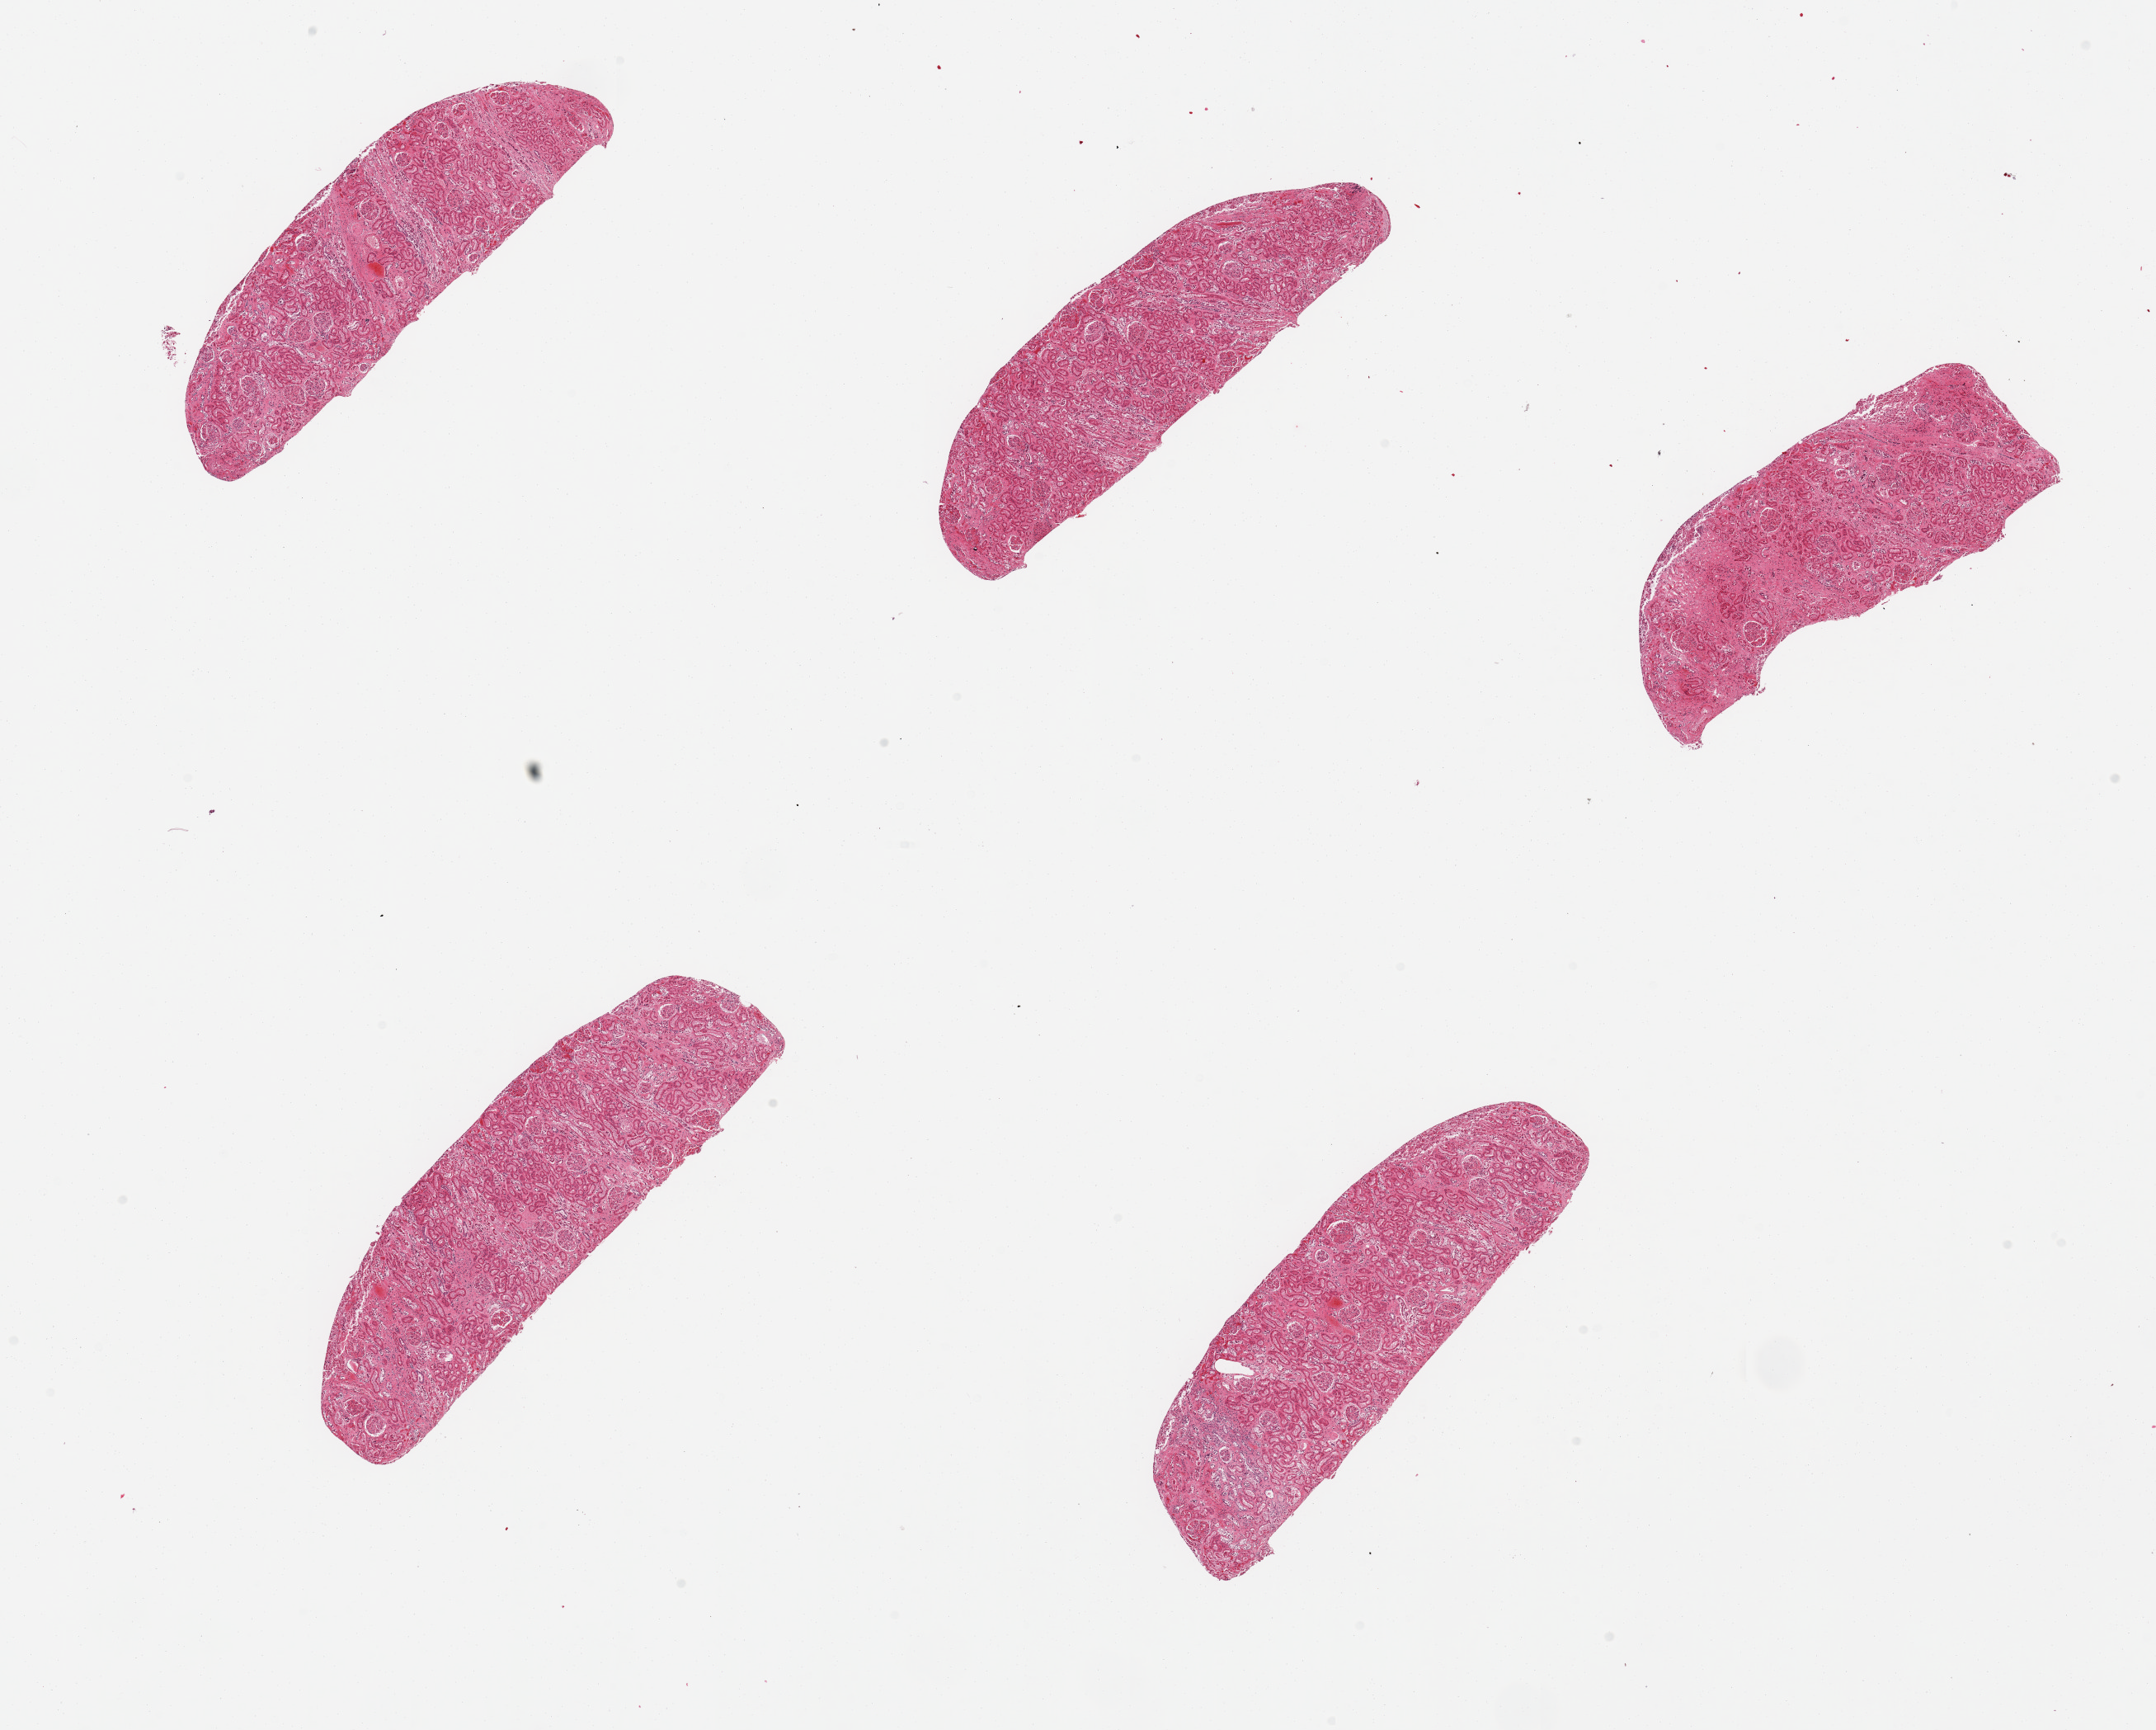
Digitized hematoxylin and eosin (H&E)-stained section, brightfield, whole scanned area (about 20.7 x 16.6 mm) shown as a low-resolution overview. PAXgene-fixed, paraffin-embedded tissue. Target tissue: renal cortex. Donor tissue sample. Donor: male.
* review note (as recorded): 5 pieces; congested cortex; grade 2 tubular autolysis